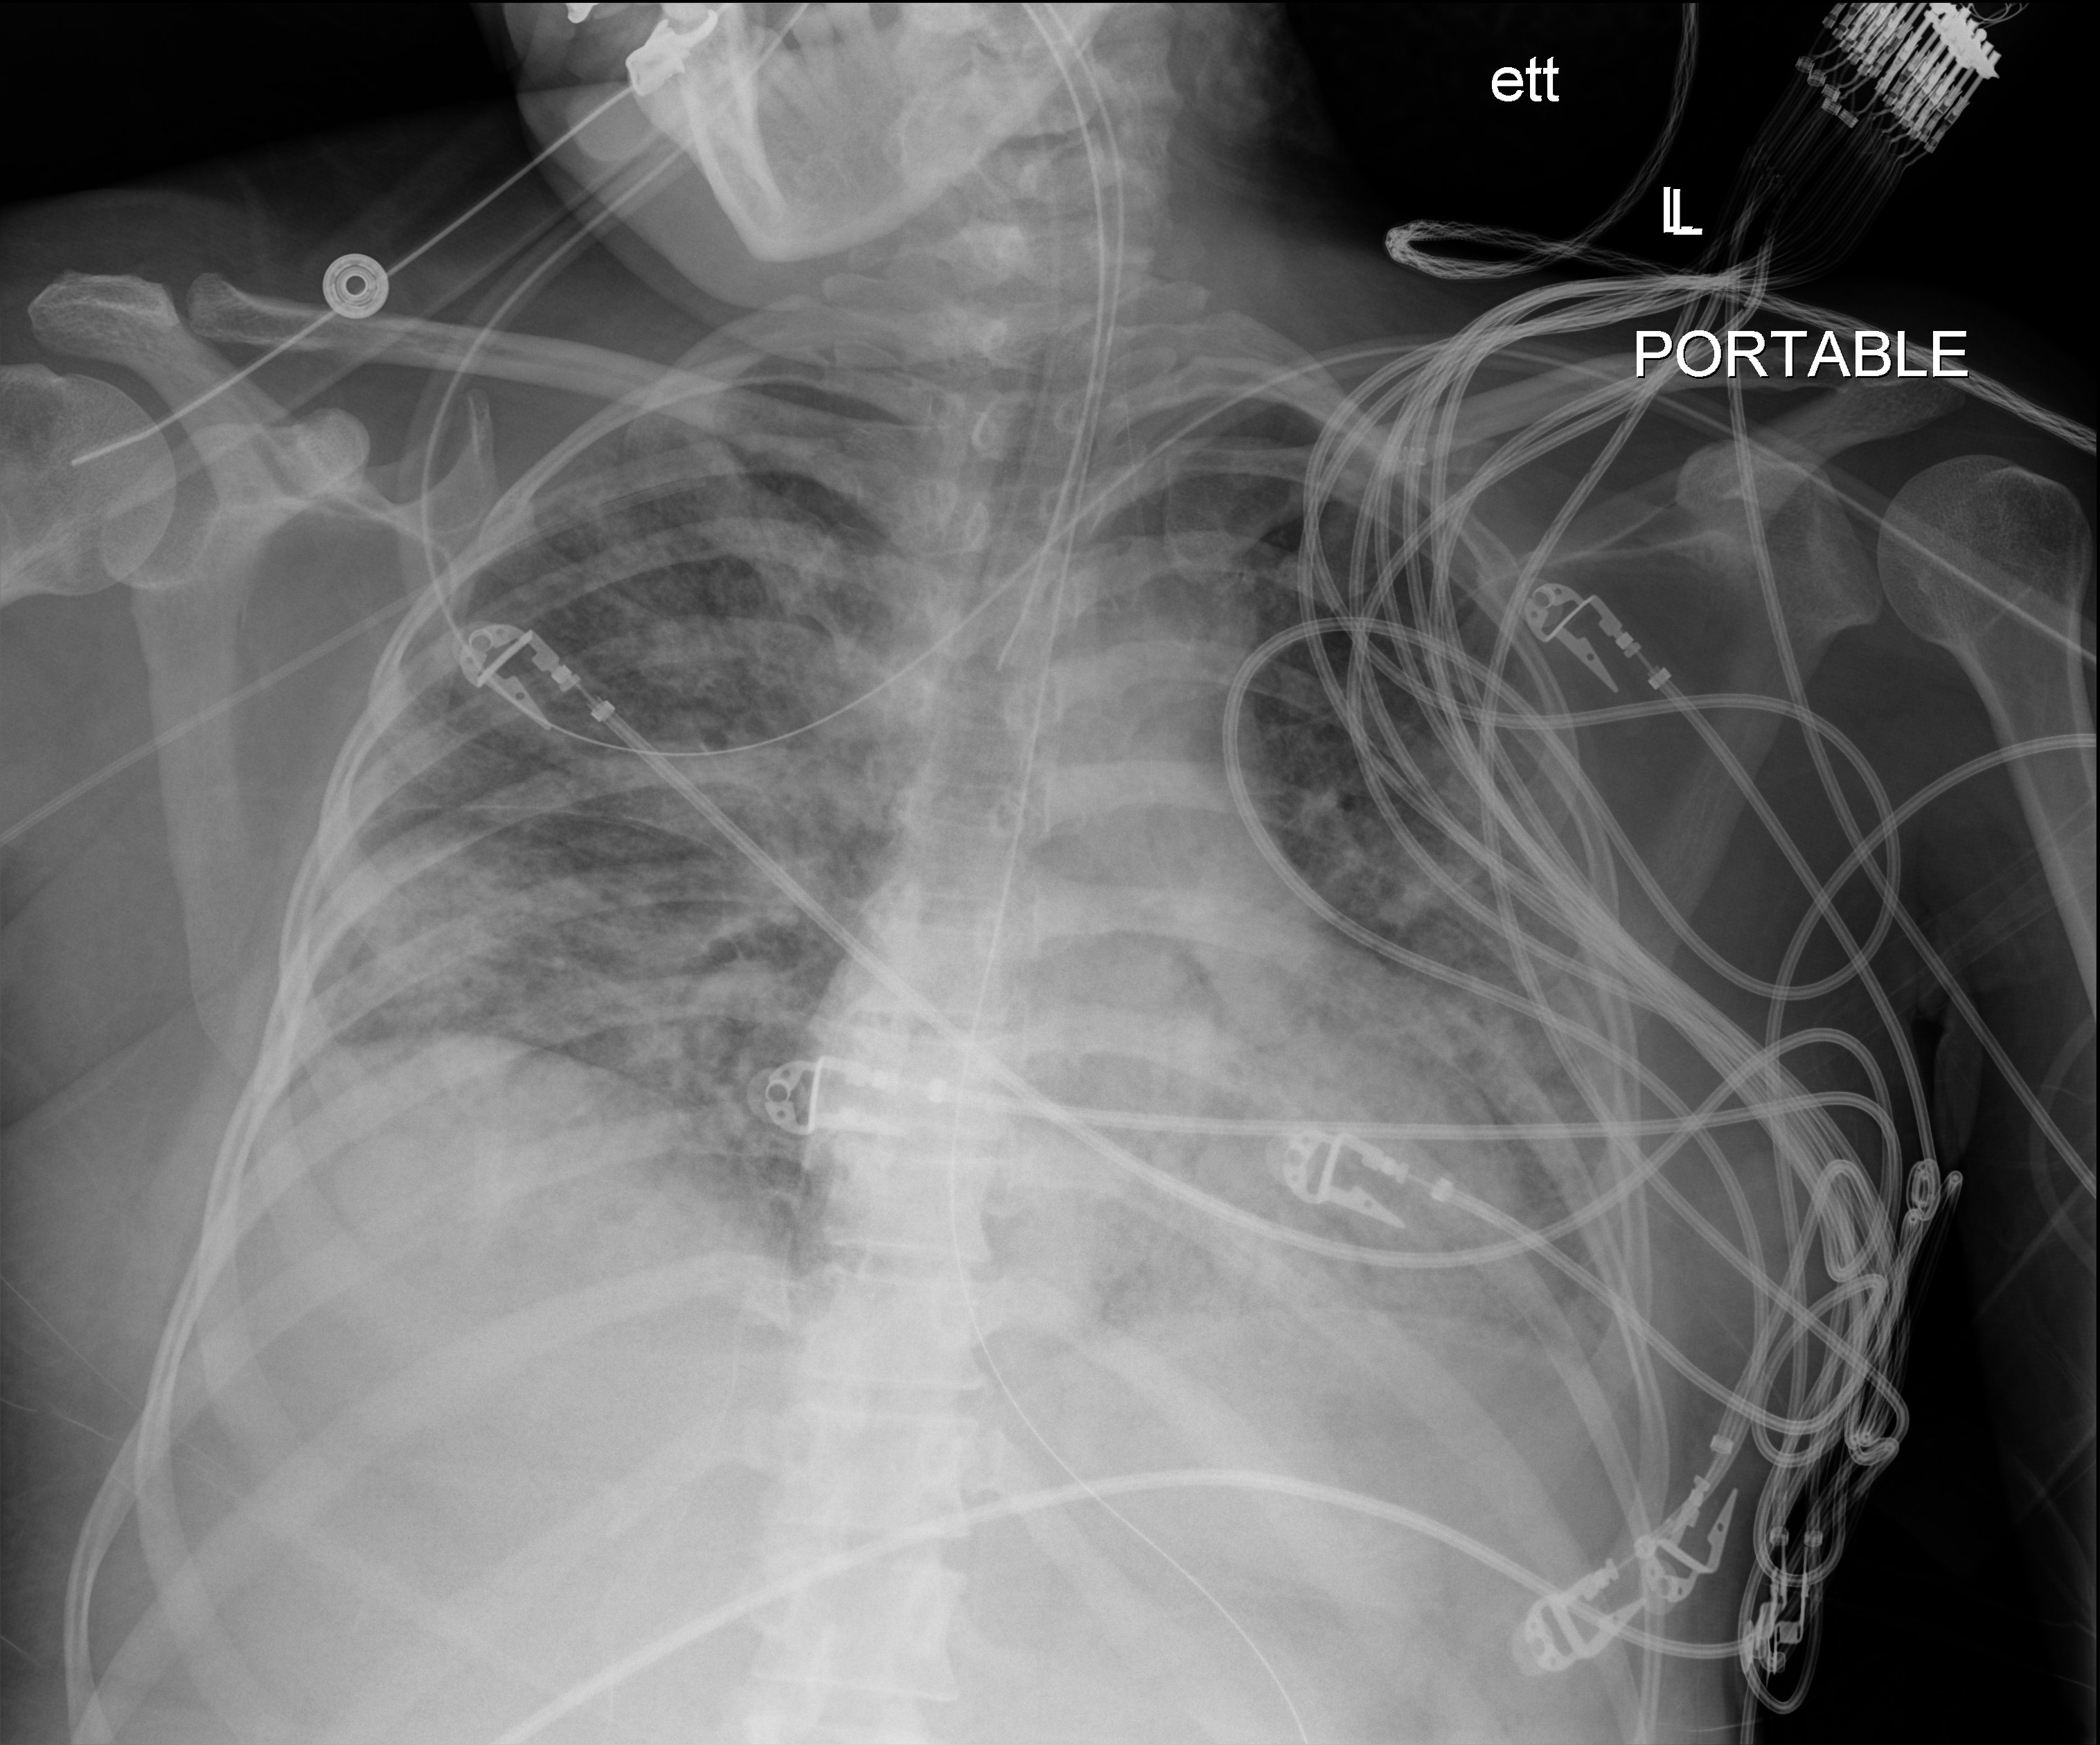
Portable chest radiograph; anteroposterior (AP) projection. Female patient hospitalised with COVID-19, age 18–59 years.
From the hospital-stay record, not from the radiograph (when in the stay this image was taken is not recorded): mechanically ventilated during this hospital stay: yes.